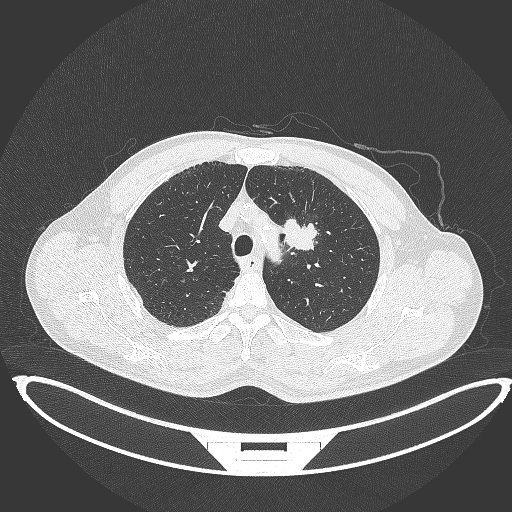
Chest CT, one axial slice. Slice 340 of 395 in the series (ordered by position). Reconstruction kernel B70f. 120 kVp. Lung window (W 1500 / L -600 HU). 1 mm slice thickness. 512 × 512 image matrix, field of view 457 × 457 mm. Patient: male, 60 years. Case-level facts recorded for this patient, not image findings: clinical TNM (as recorded): T2a N0 M0; histopathological grade: G1-G2.
Structures marked on this image (bounding box drawn by a radiologist):
- lung tumour (recorded histology: squamous cell carcinoma): bounding box <279,213,320,252> (left, top, right, bottom; pixels)